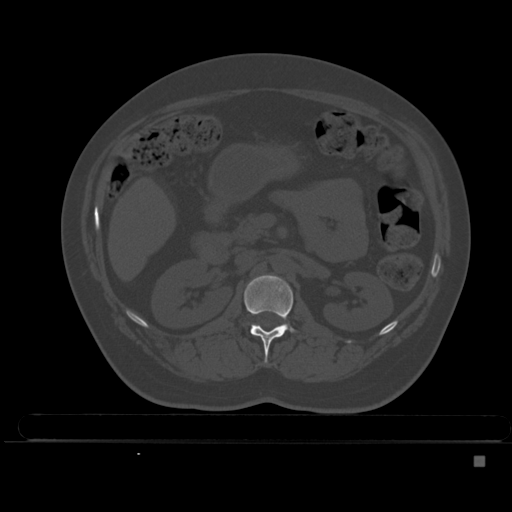
CT including the spine, one axial slice; position 191 of 495 along the scan axis; bone window (W 1800 / L 400 HU); 1.5 mm slice thickness; 512 × 512 image matrix, field of view 404 × 404 mm. Female patient, age 33 years. From the clinical record (not read from this slice): primary cancer: breast.
Outlined on this slice (semi-automatically segmented with operator editing):
- L1 vertebra: bounding box [x1, y1, x2, y2] px = [244, 275, 297, 363]